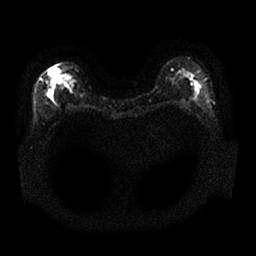
Breast MRI, one axial slice; position 14 of 25 along the scan axis; diffusion-weighted series; image 2 of 4 stored at this slice position (different b-values; order by instance number); 1.5 T; 256 × 256 image matrix. Female patient.
Structures marked on this image (outlined manually by an expert reader):
- tumour on diffusion-weighted imaging: box from (x=47, y=67) to (x=59, y=100) px